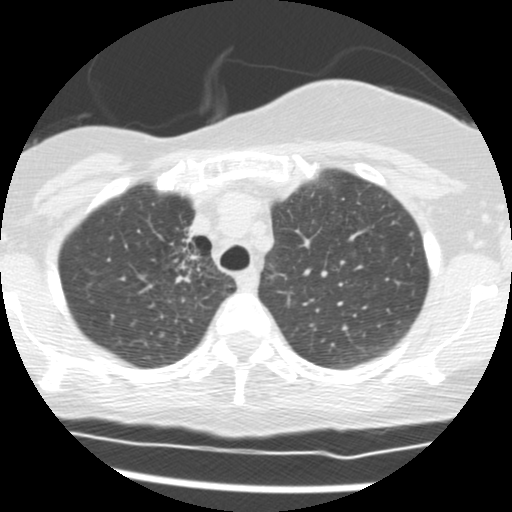
Low-dose screening chest CT, axial slice; second screening round (one year after baseline); lung window (W 1500 / L -600 HU); 2.5 mm slice thickness. Female, age 56 years at enrolment.
Expert reader's lesion annotation, bounding box <155,222,218,290> (left, top, right, bottom; pixels). The screening reader recorded 2 non-calcified nodules or masses ≥4 mm on this exam (right middle lobe, right lower lobe); which of them this box marks is not recorded. Participant outcome: lung cancer diagnosed 675 days after this screen (after the third annual screen) — adenocarcinoma, NOS, right upper lobe, stage IIIB (AJCC 6th edition), 8 mm at pathology.